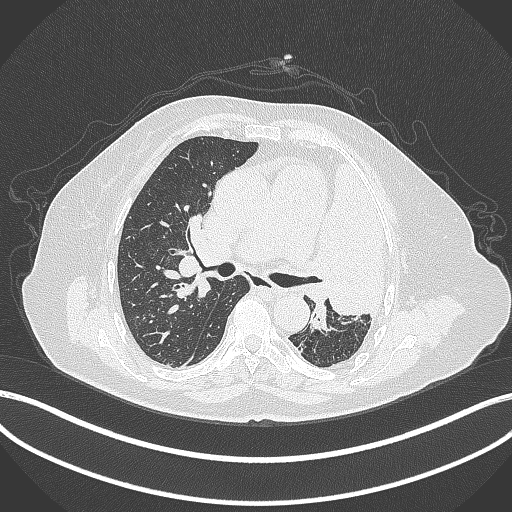
Chest CT, one axial slice. Slice 234 of 399 in the series (ordered by position). Reconstruction kernel B70f. Lung window (W 1500 / L -600 HU). 512 × 512 image matrix, field of view 400 × 400 mm. Patient: female, 75 years. From the clinical record (not read from this slice): clinical TNM (as recorded): T3 N3 M1.
Structures marked on this image (bounding box drawn by a radiologist):
- lung tumour (recorded histology: adenocarcinoma): bounding box (x1, y1, x2, y2) in pixels: (311, 152, 390, 318)